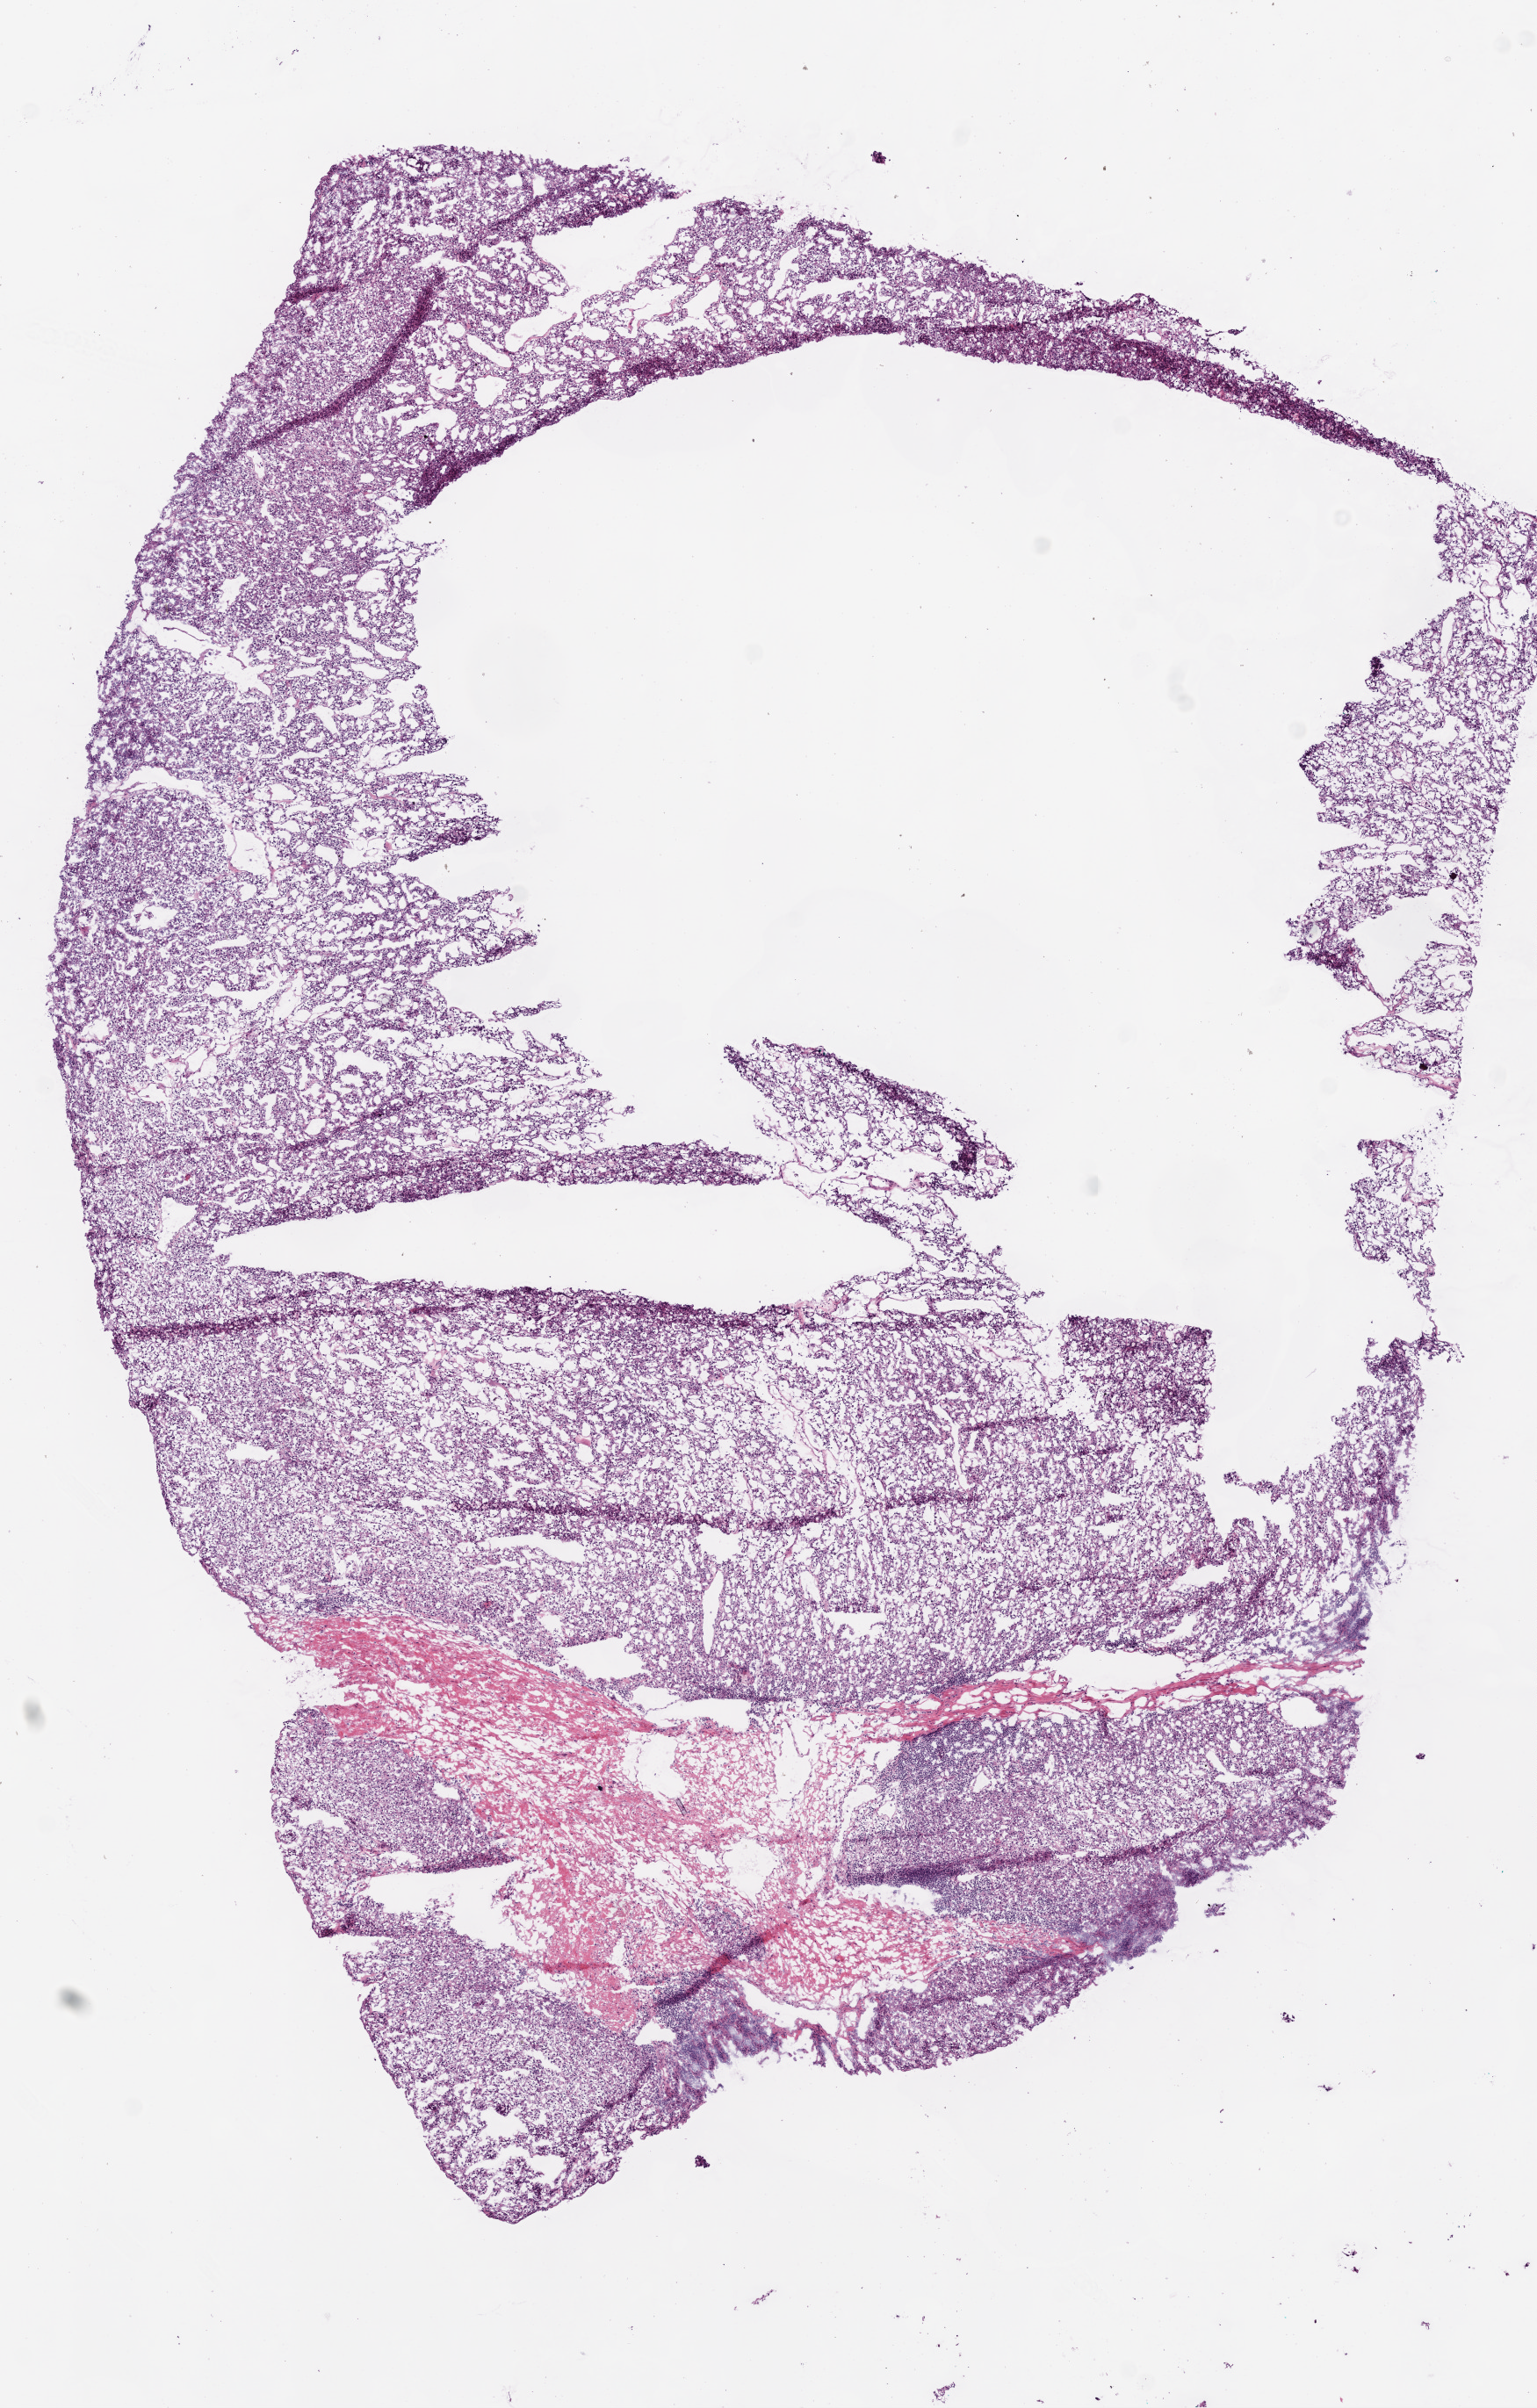
Digitized Hematoxylin and eosin (H&E) stained tissue section (whole slide), shown as a low-resolution overview of the whole scanned area (about 7.0 x 11.0 mm); frozen section; primary tumour sample from the kidney. Patient: female, age at initial diagnosis 54 years. Histologic grade: G2 (moderately differentiated). Pathologist review of this section (percent, as recorded): tumour cells 90%, tumour nuclei 80%, normal cells 0%, stromal cells 10%, necrosis 0%.
Pathologic diagnosis: Clear cell adenocarcinoma, NOS. TNM: T2 N0 M0. AJCC pathologic stage: II. Lymph nodes positive (case pathology): 0 of 5 examined.